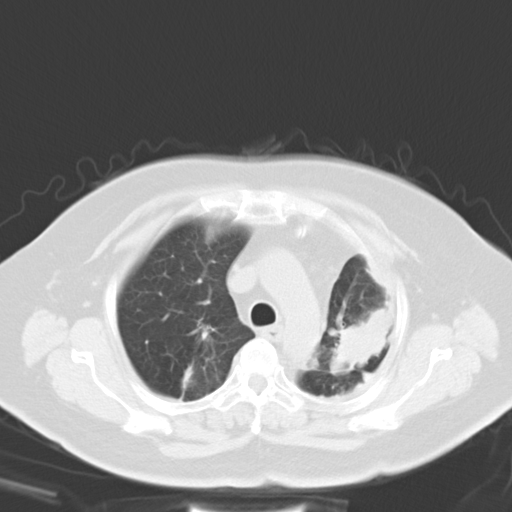
Chest CT, one axial slice; position 22 of 29 along the scan axis; reconstruction kernel B40f; 120 kVp; lung window (W 1500 / L -600 HU); 8 mm slice thickness; 512 × 512 image matrix, field of view 347 × 347 mm. Patient: female, 69 years. Case-level facts recorded for this patient, not image findings: clinical TNM (as recorded): T3 N0 M0.
Structures marked on this image (rectangle marked by the reading radiologist):
- lung tumour (recorded histology: adenocarcinoma): bounding box (x1, y1, x2, y2) in pixels: (334, 297, 392, 373)